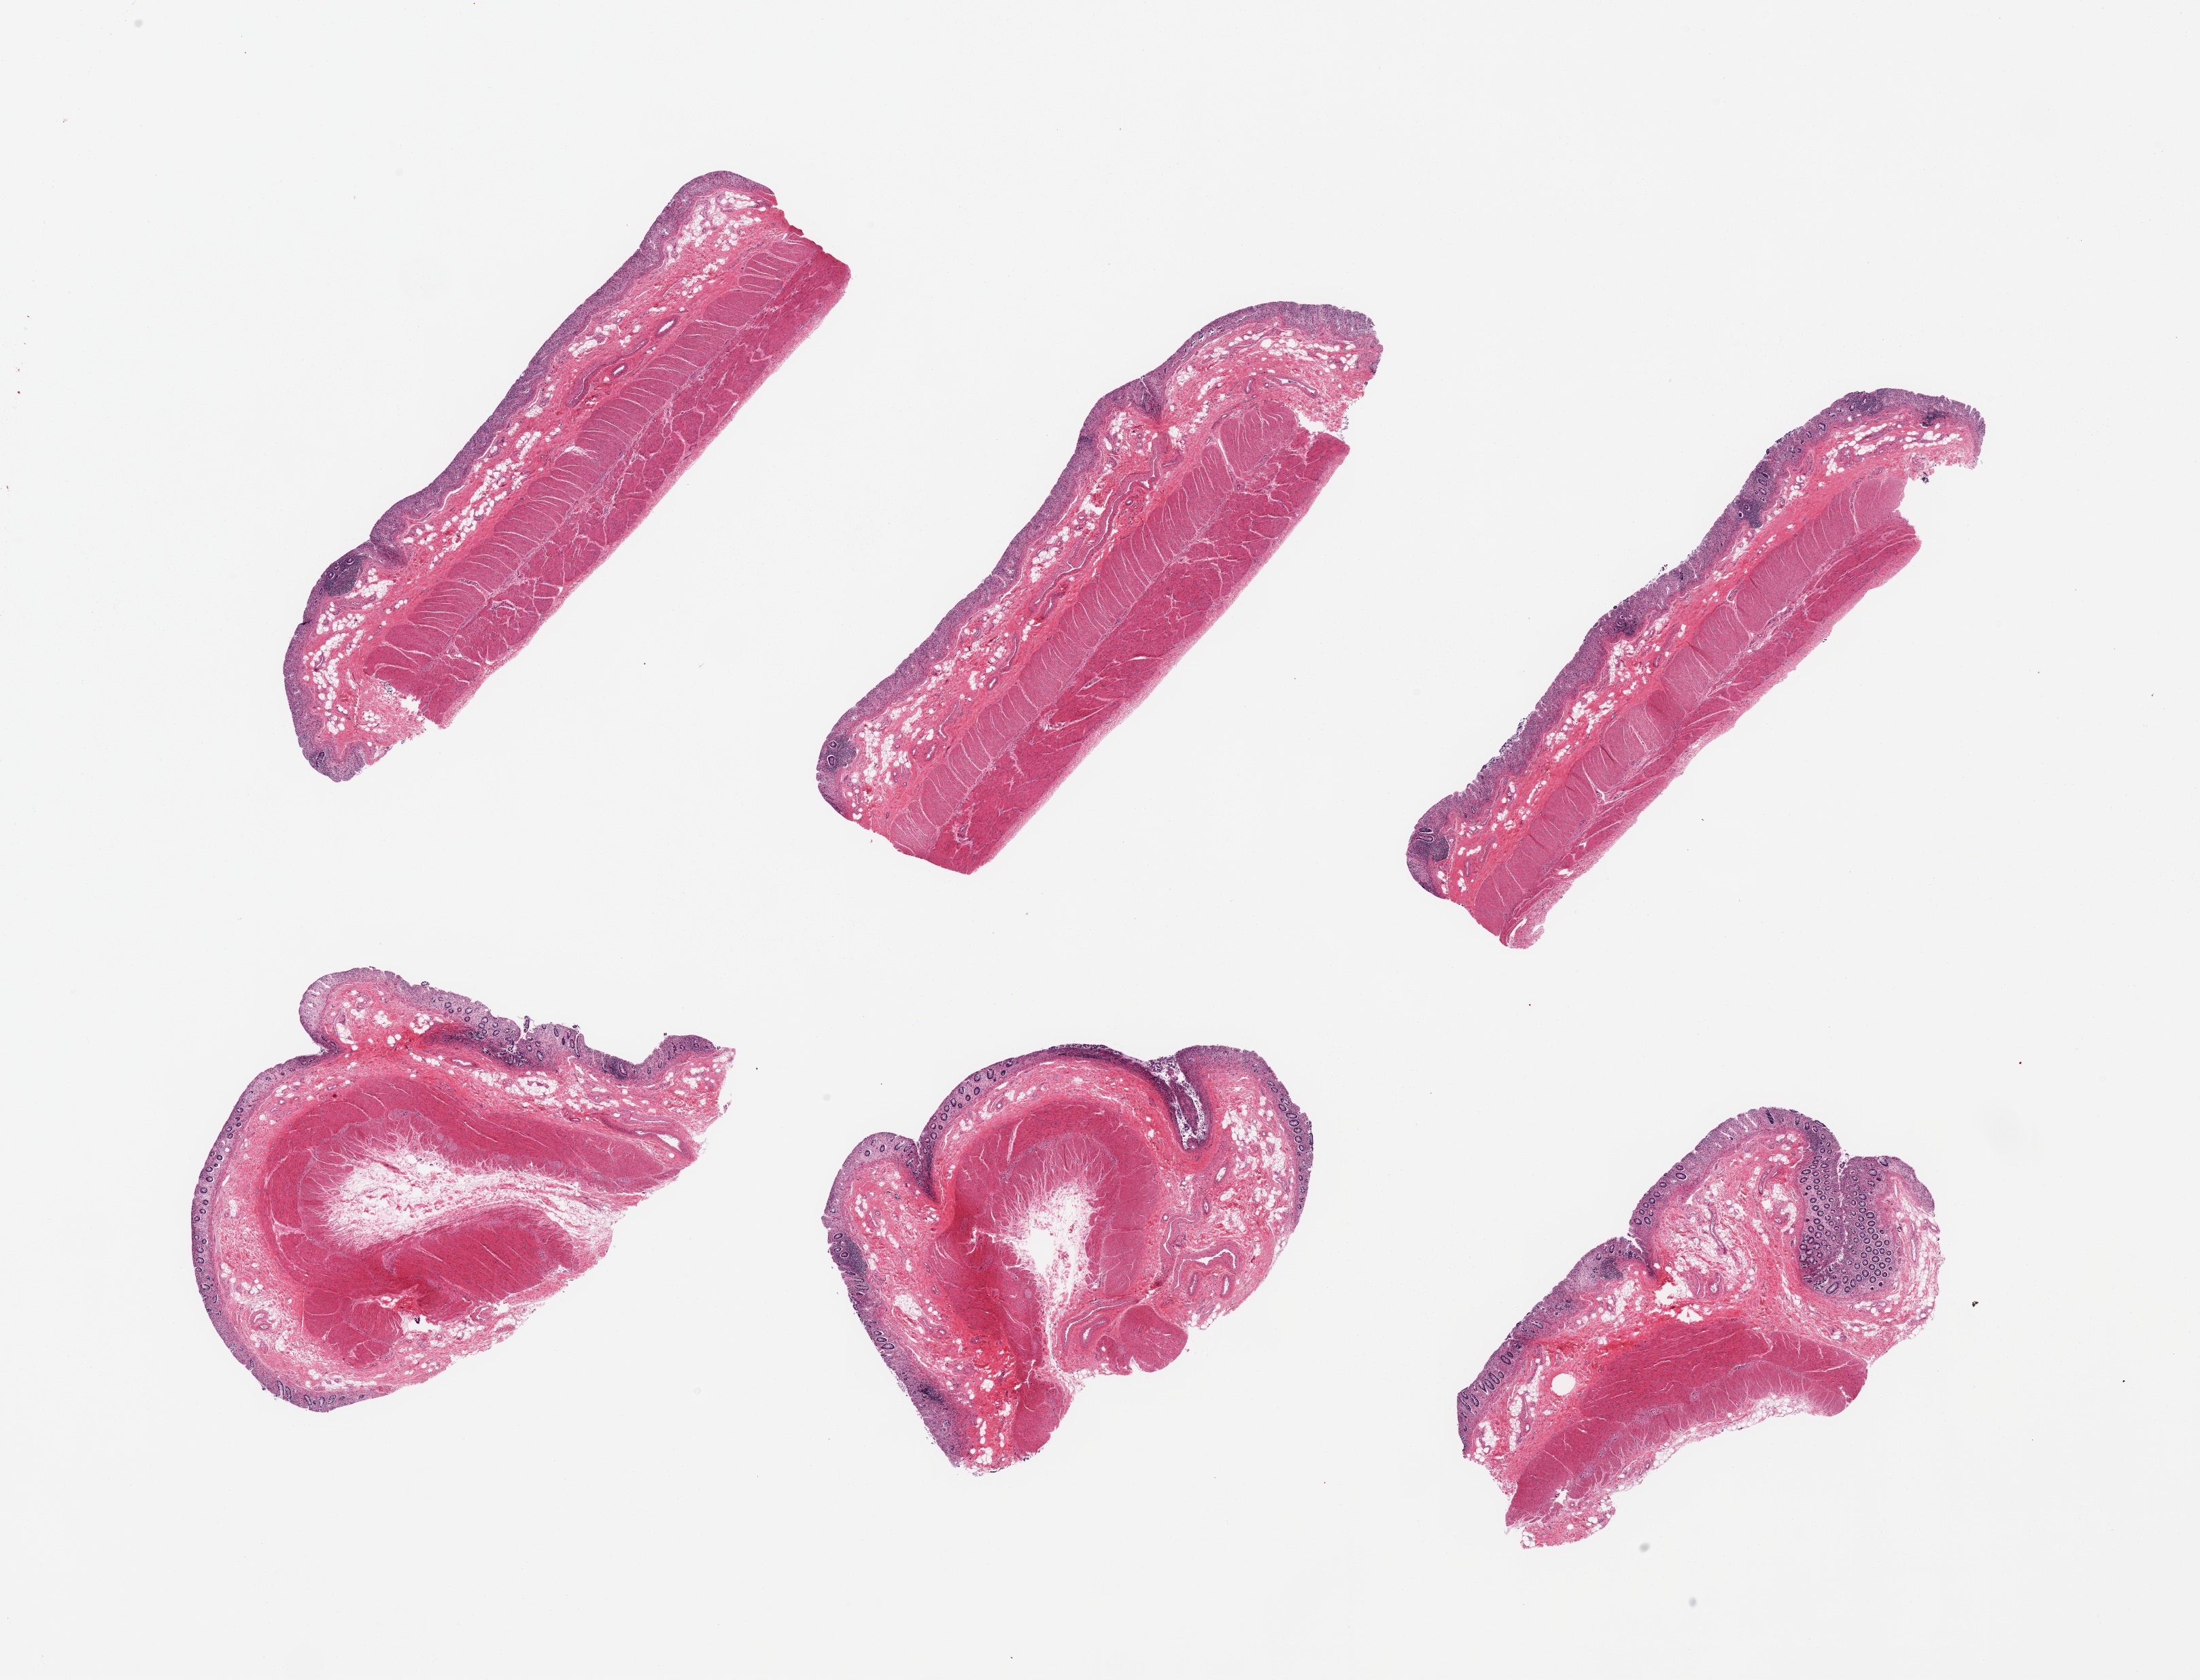
Digitized hematoxylin and eosin (H&E)-stained section, brightfield, a low-resolution overview of the entire scanned area, about 25.6 x 19.5 mm. PAXgene-fixed, paraffin-embedded tissue. Sampled site (target tissue): transverse colon. Donor tissue sample. Donor sex: female.
Reviewer comment on this tissue sample: 6 pieces; moderate to severe autolysis of colonic mucosa; preserved muscularis.